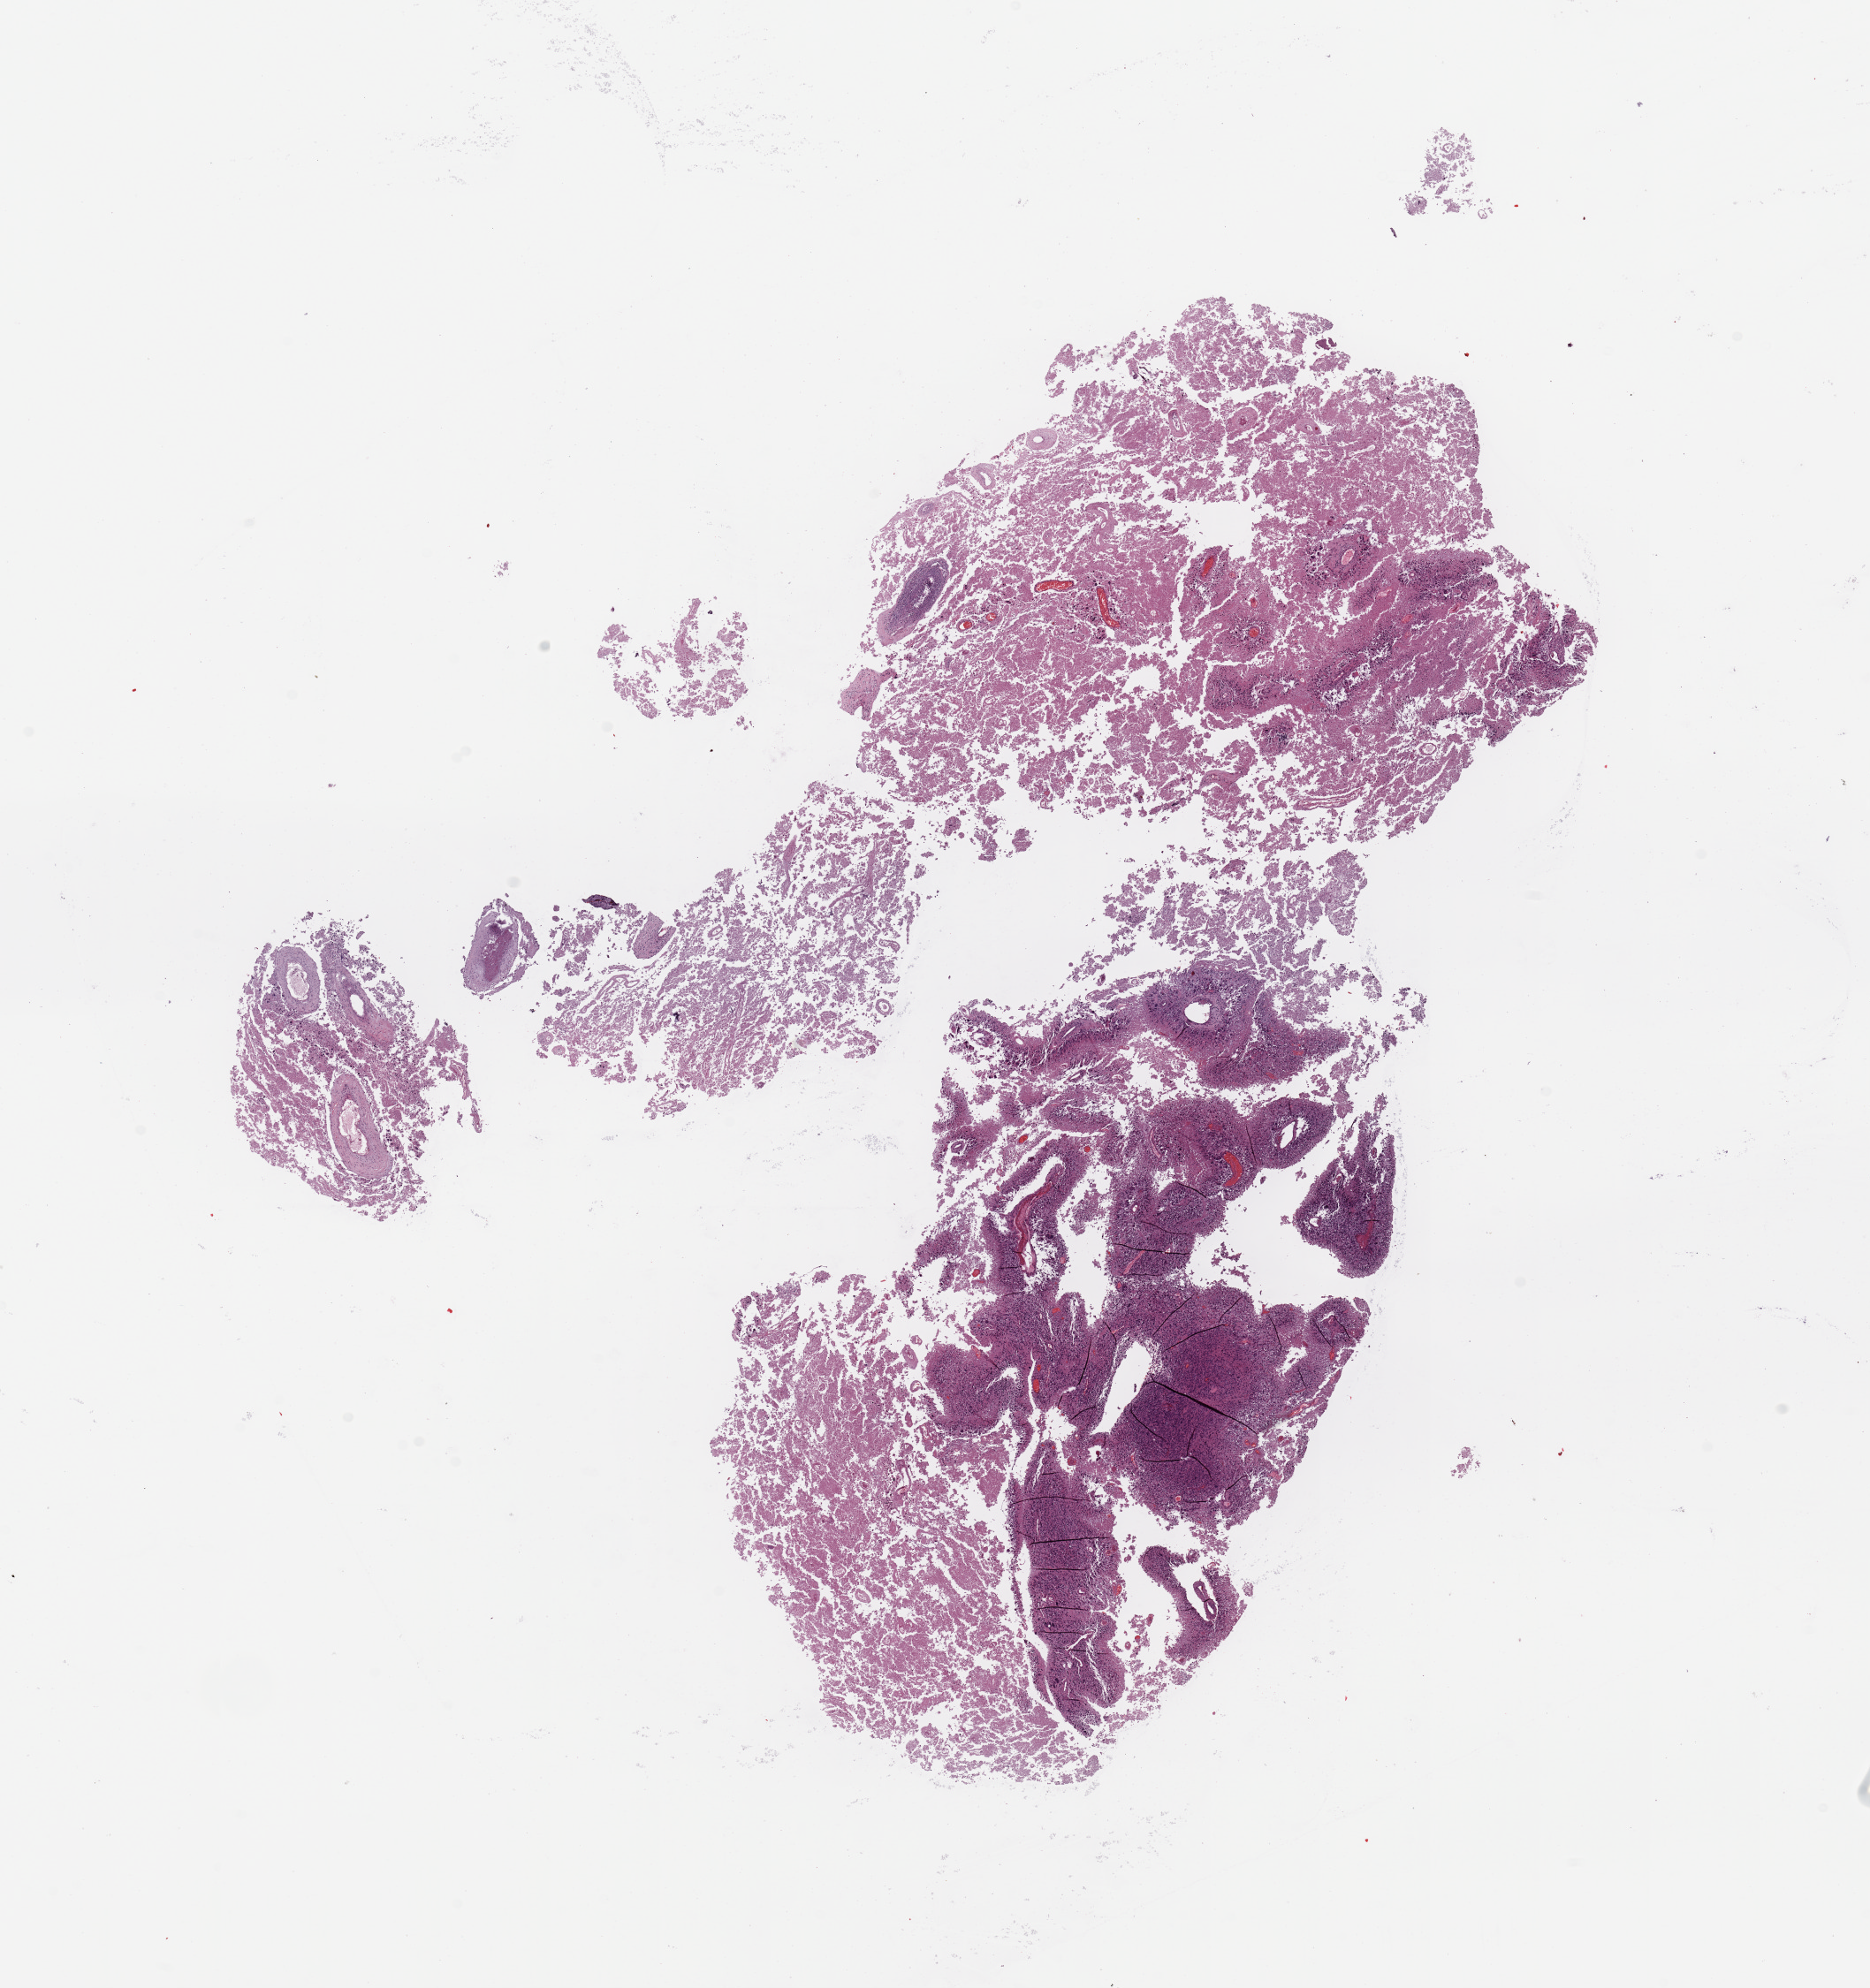
Whole-slide histology image, H&E — a low-resolution overview of the entire scanned area, about 16.7 x 17.8 mm (acquisition: 20x scan). Tumour tissue sample, brain. 61-year-old female patient.
Primary tumour site (as recorded): frontal lobe. Histologic diagnosis: Glioblastoma.